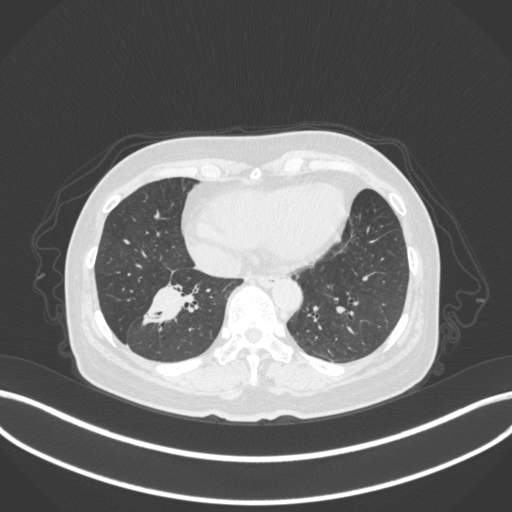
Chest CT, one axial slice. Position 125 of 429 along the scan axis. Lung window (W 1500 / L -600 HU). 1 mm slice thickness. 512 × 512 image matrix, field of view 400 × 400 mm. Female patient, age 67 years. From the clinical record (not read from this slice): clinical TNM (as recorded): T1c N1 M0; histopathological grade: G2-3.
Structures marked on this image (bounding box drawn by a radiologist):
- lung tumour (recorded histology: adenocarcinoma): bounding box <140,273,200,332> (left, top, right, bottom; pixels)